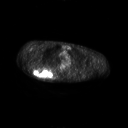
FDG PET of an extremity soft-tissue mass (from a PET/CT study), one axial slice. Slice 186 of 267 in the series (ordered by position). 128 × 128 image matrix, field of view 700 × 700 mm. Patient: male, 61 years. Case-level facts recorded for this patient, not image findings: histological type: pleiomorphic spindle cell undifferentiated; grade: high; site of the primary tumour: right parascapusular.
Structures marked on this image (expert contour drawn on MRI and transferred to this co-registered scan by the dataset authors):
- gross tumour volume including surrounding oedema: box from (x=33, y=67) to (x=58, y=79) px
- gross tumour volume (mass): (x=33, y=67)–(x=54, y=78)